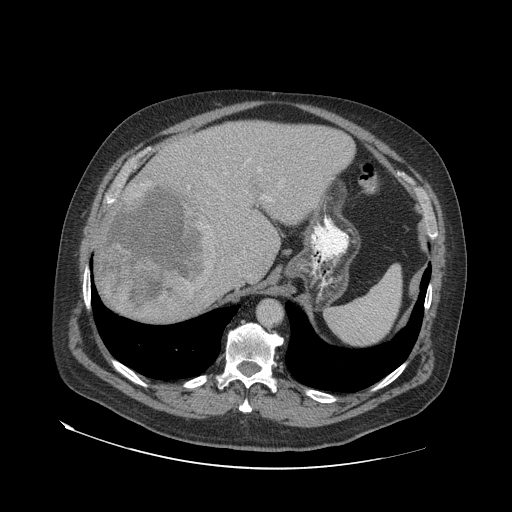
Contrast-enhanced abdominal CT (liver protocol), one axial slice; position 52 of 79 along the scan axis; reconstruction kernel STANDARD; 140 kVp; soft-tissue window (W 400 / L 40 HU); 2.5 mm slice thickness; 512 × 512 image matrix, field of view 480 × 480 mm. From the clinical record (not read from this slice): diagnosis: hepatocellular carcinoma (patient treated with transarterial chemoembolisation; whether this scan precedes or follows treatment is not stated here); TNM stage (as recorded): Stage-IVA; Child-Pugh class: A; tumour nodularity: multinodular.
Annotated regions visible in this slice (semi-automatically segmented with operator editing):
- abdominal aorta: bounding box <258,300,281,325> (left, top, right, bottom; pixels)
- liver parenchyma outside the tumour (the mass and vessels are separate outlines, so this box may not span the whole liver): <94,120,354,316>
- mass: <98,181,219,324>
- liver vessels: <188,159,271,200>